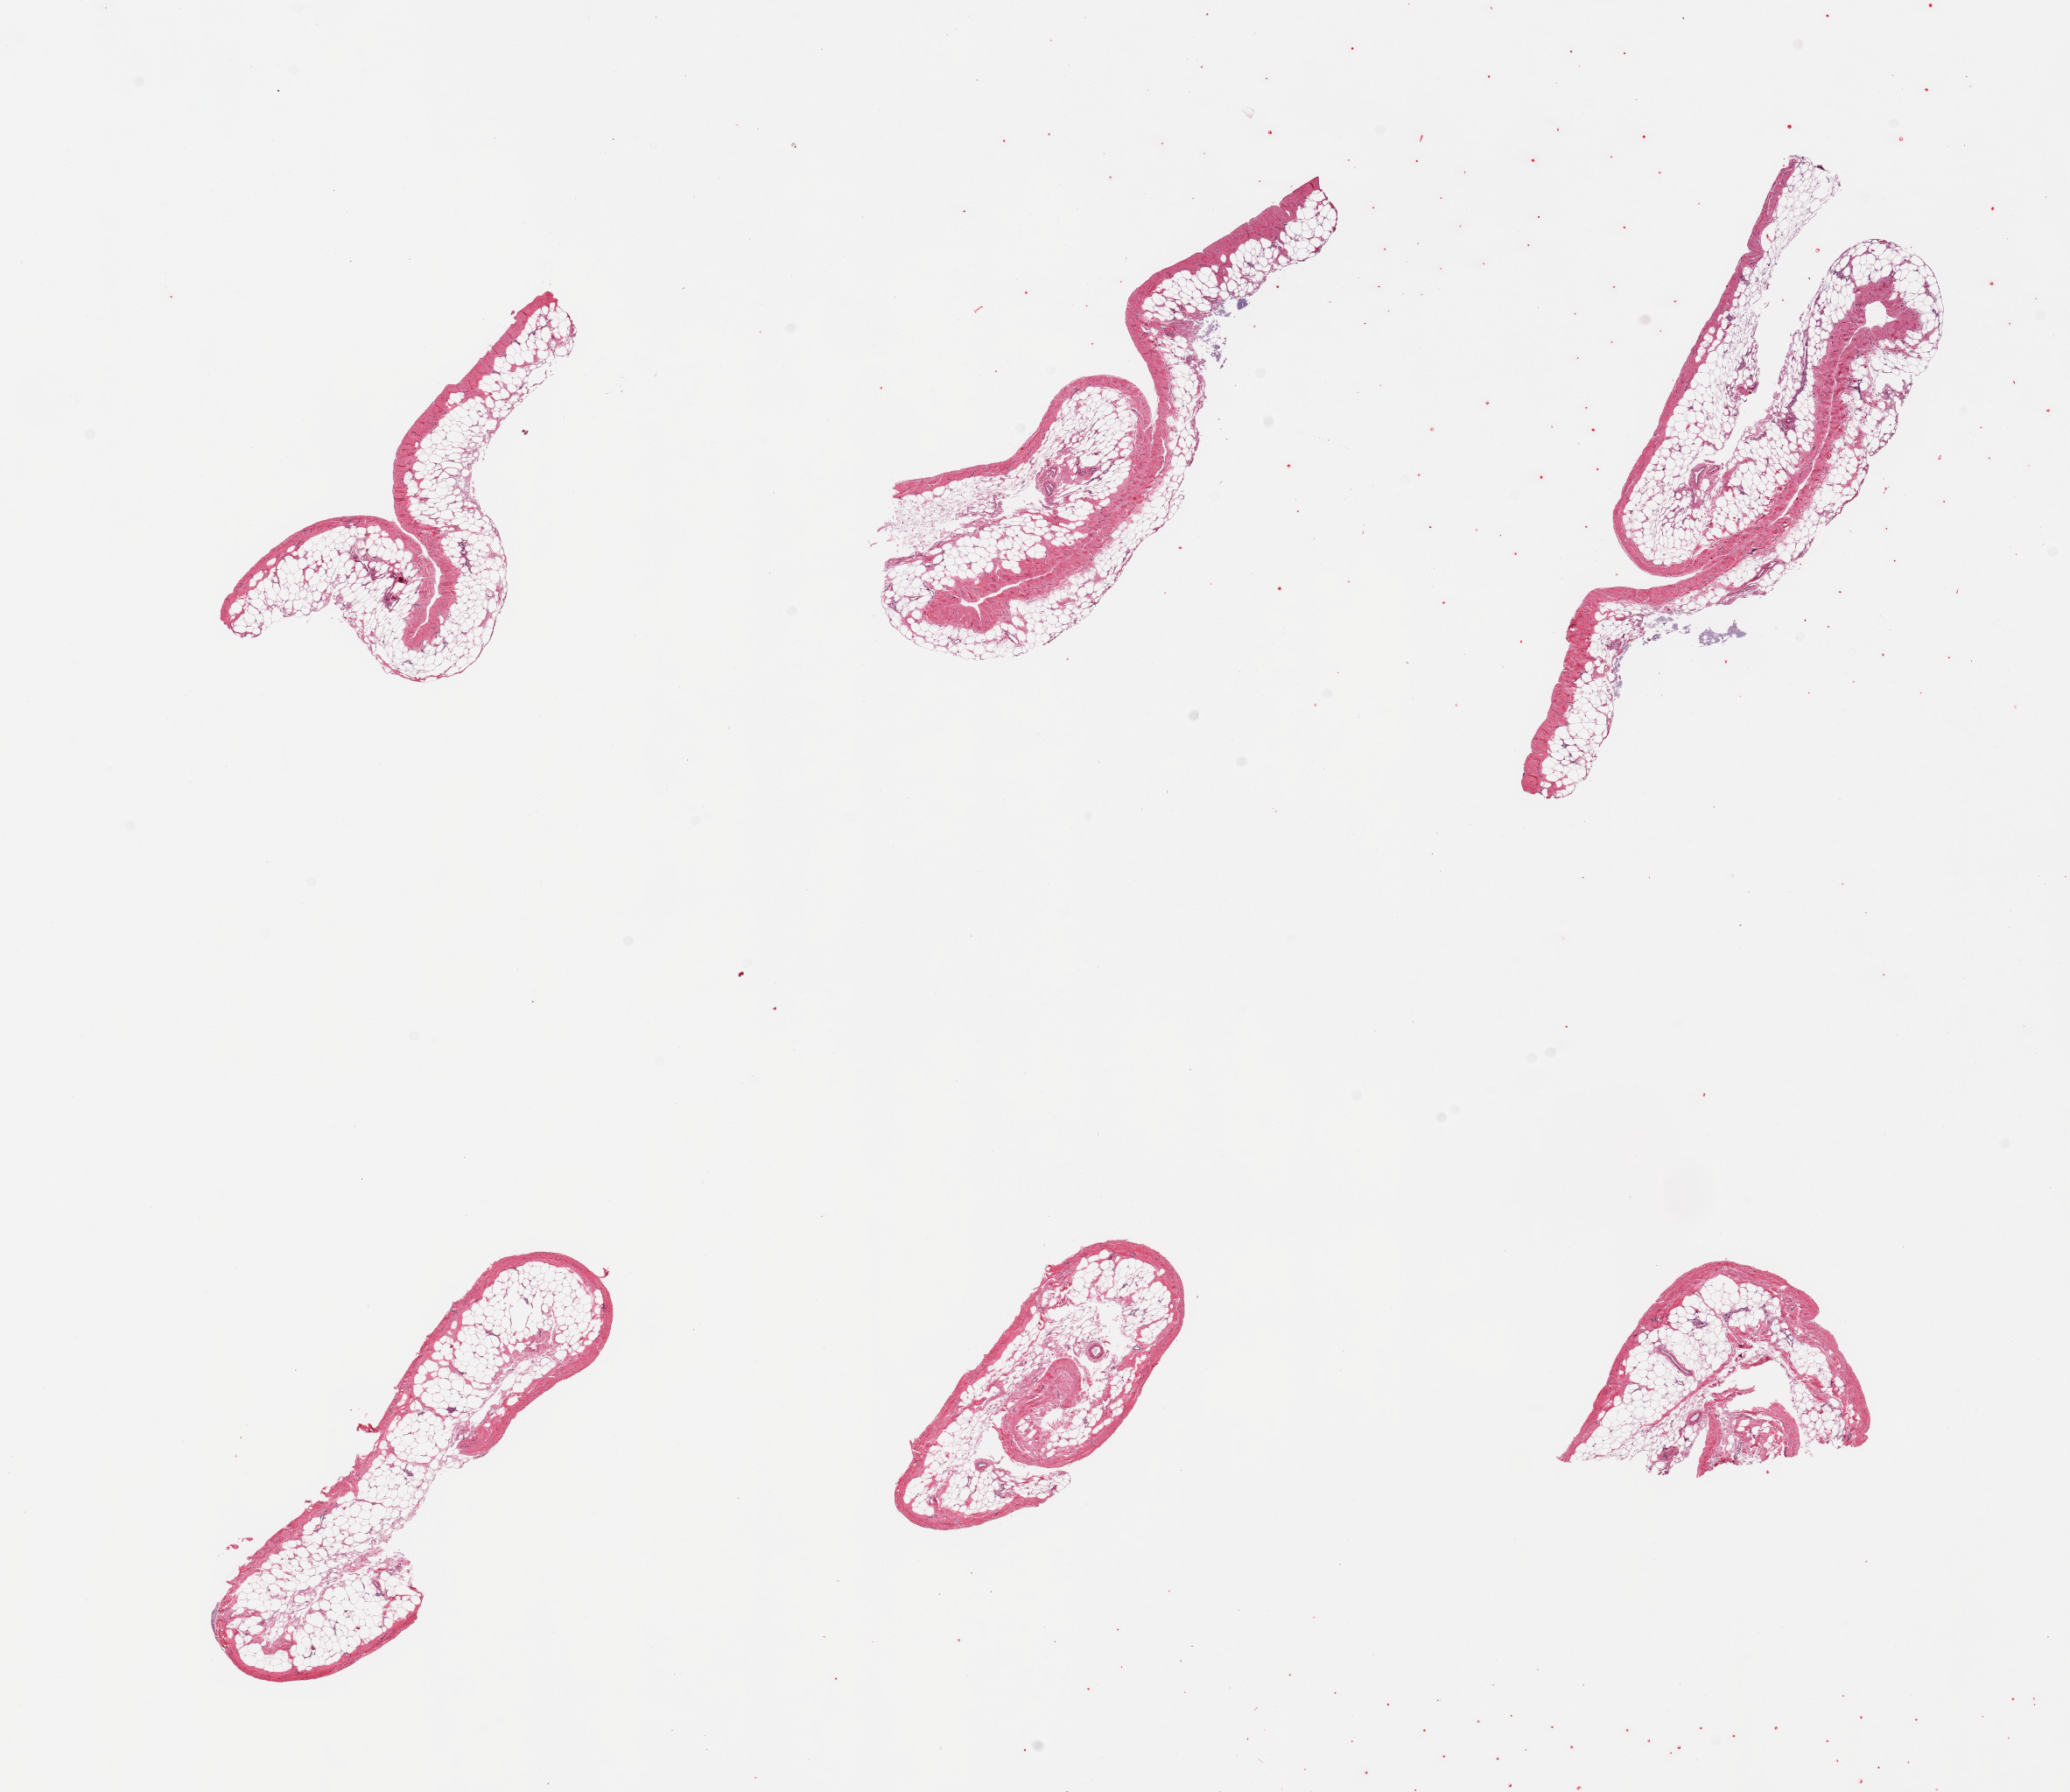
Digitized hematoxylin and eosin (H&E)-stained section — a low-resolution overview of the entire scanned area, about 18.7 x 16.2 mm. Donor: male.
Specimen: PAXgene-fixed, paraffin-embedded tissue; target tissue: ileum; tissue donor sample.